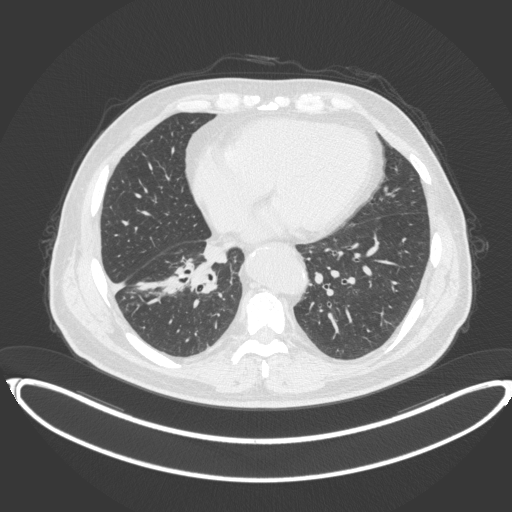
Chest CT, one axial slice; position 152 of 383 along the scan axis; 120 kVp; lung window (W 1500 / L -600 HU); 1 mm slice thickness; 512 × 512 image matrix, field of view 448 × 448 mm. Patient: male, 61 years. From the clinical record (not read from this slice): clinical TNM (as recorded): T1b N1 M0.
Structures marked on this image (bounding box drawn by a radiologist):
- lung tumour (recorded histology: squamous cell carcinoma): bounding box (x1, y1, x2, y2) in pixels: (164, 256, 218, 298)